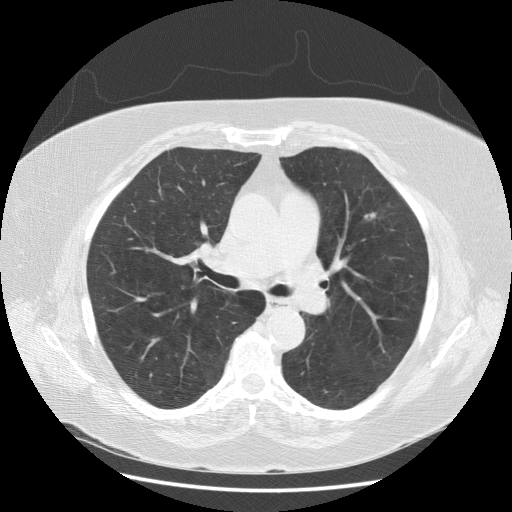
Low-dose screening chest CT, one axial slice. Slice 98 of 164 in the series (ordered by position). 120 kVp. Lung window (W 1500 / L -600 HU). 512 × 512 image matrix.
Outlined on this slice (expert manual segmentation):
- lesion 1 (tumor, upper lobe of left lung): box from (x=365, y=213) to (x=376, y=219) px